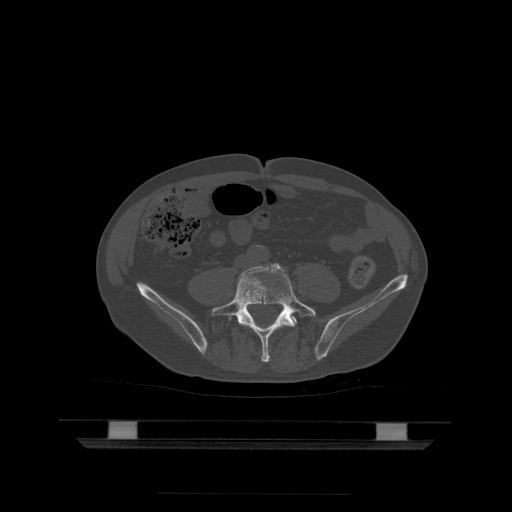
CT including the spine, one axial slice; bone window (W 1800 / L 400 HU); 1.25 mm slice thickness; 512 × 512 image matrix, field of view 436 × 436 mm. Patient age 68 years. Case-level facts recorded for this patient, not image findings: primary cancer: urothelial.
Outlined on this slice (semi-automatic segmentation, software-assisted and operator-edited):
- L5 vertebra: bounding box <211,264,317,362> (left, top, right, bottom; pixels)